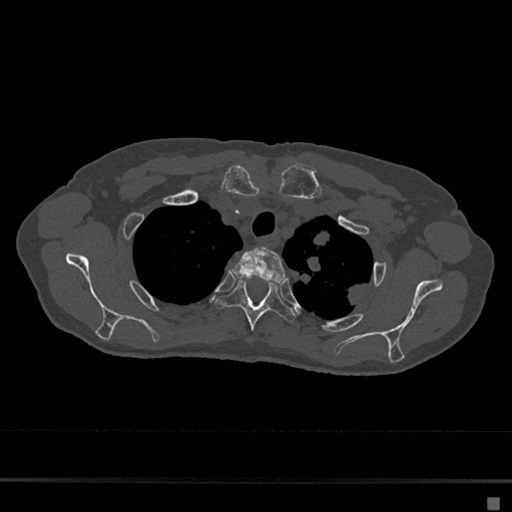
CT including the spine, one axial slice. Position 551 of 797 along the scan axis. Reconstruction kernel Br40s/3. 120 kVp. Bone window (W 1800 / L 400 HU). 512 × 512 image matrix. Female patient, age 68 years. From the clinical record (not read from this slice): primary cancer: renal.
Annotated regions visible in this slice (semi-automatic segmentation, software-assisted and operator-edited):
- T2 vertebra: bounding box (x1, y1, x2, y2) in pixels: (232, 247, 287, 282)
- T3 vertebra: (218, 279, 296, 331)